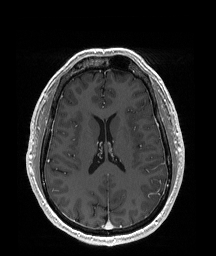
Brain MRI from a brain-tumour surgery series, one axial slice. T1-weighted post-contrast. 1 mm slice thickness. 216 × 256 image matrix. Case-level facts recorded for this patient, not image findings: histopathology: Glioblastoma; WHO grade: 4; IDH mutation: no; tumour location: Left Temporal Parietal.
Annotated regions visible in this slice (manually delineated by an expert):
- tumour: bounding box <141,178,166,211> (left, top, right, bottom; pixels)